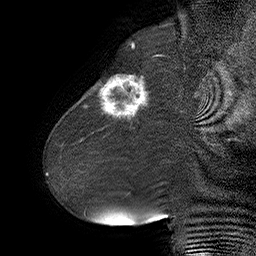
Breast MRI (dynamic contrast-enhanced), one sagittal slice. Position 18 of 55 along the scan axis. Dynamic contrast-enhanced series, time point 2 of 6 at this slice position (early post-contrast). 1.5 T. TE 4.5 ms, TR 32.4 ms. 256 × 256 image matrix. Female patient. Case-level facts recorded for this patient, not image findings: setting: breast cancer imaged before/during neoadjuvant chemotherapy; receptor status: HER2-positive.
Structures marked on this image (semi-automatic segmentation, software-assisted and operator-edited):
- analysis volume of interest (the breast-tissue region the enhancement analysis was run in; not a lesion): bounding box [x1, y1, x2, y2] px = [80, 64, 163, 134]
- tumour enhancement mask (voxels above the 100 % enhancement threshold inside the analysis volume of interest): [83, 76, 147, 117]